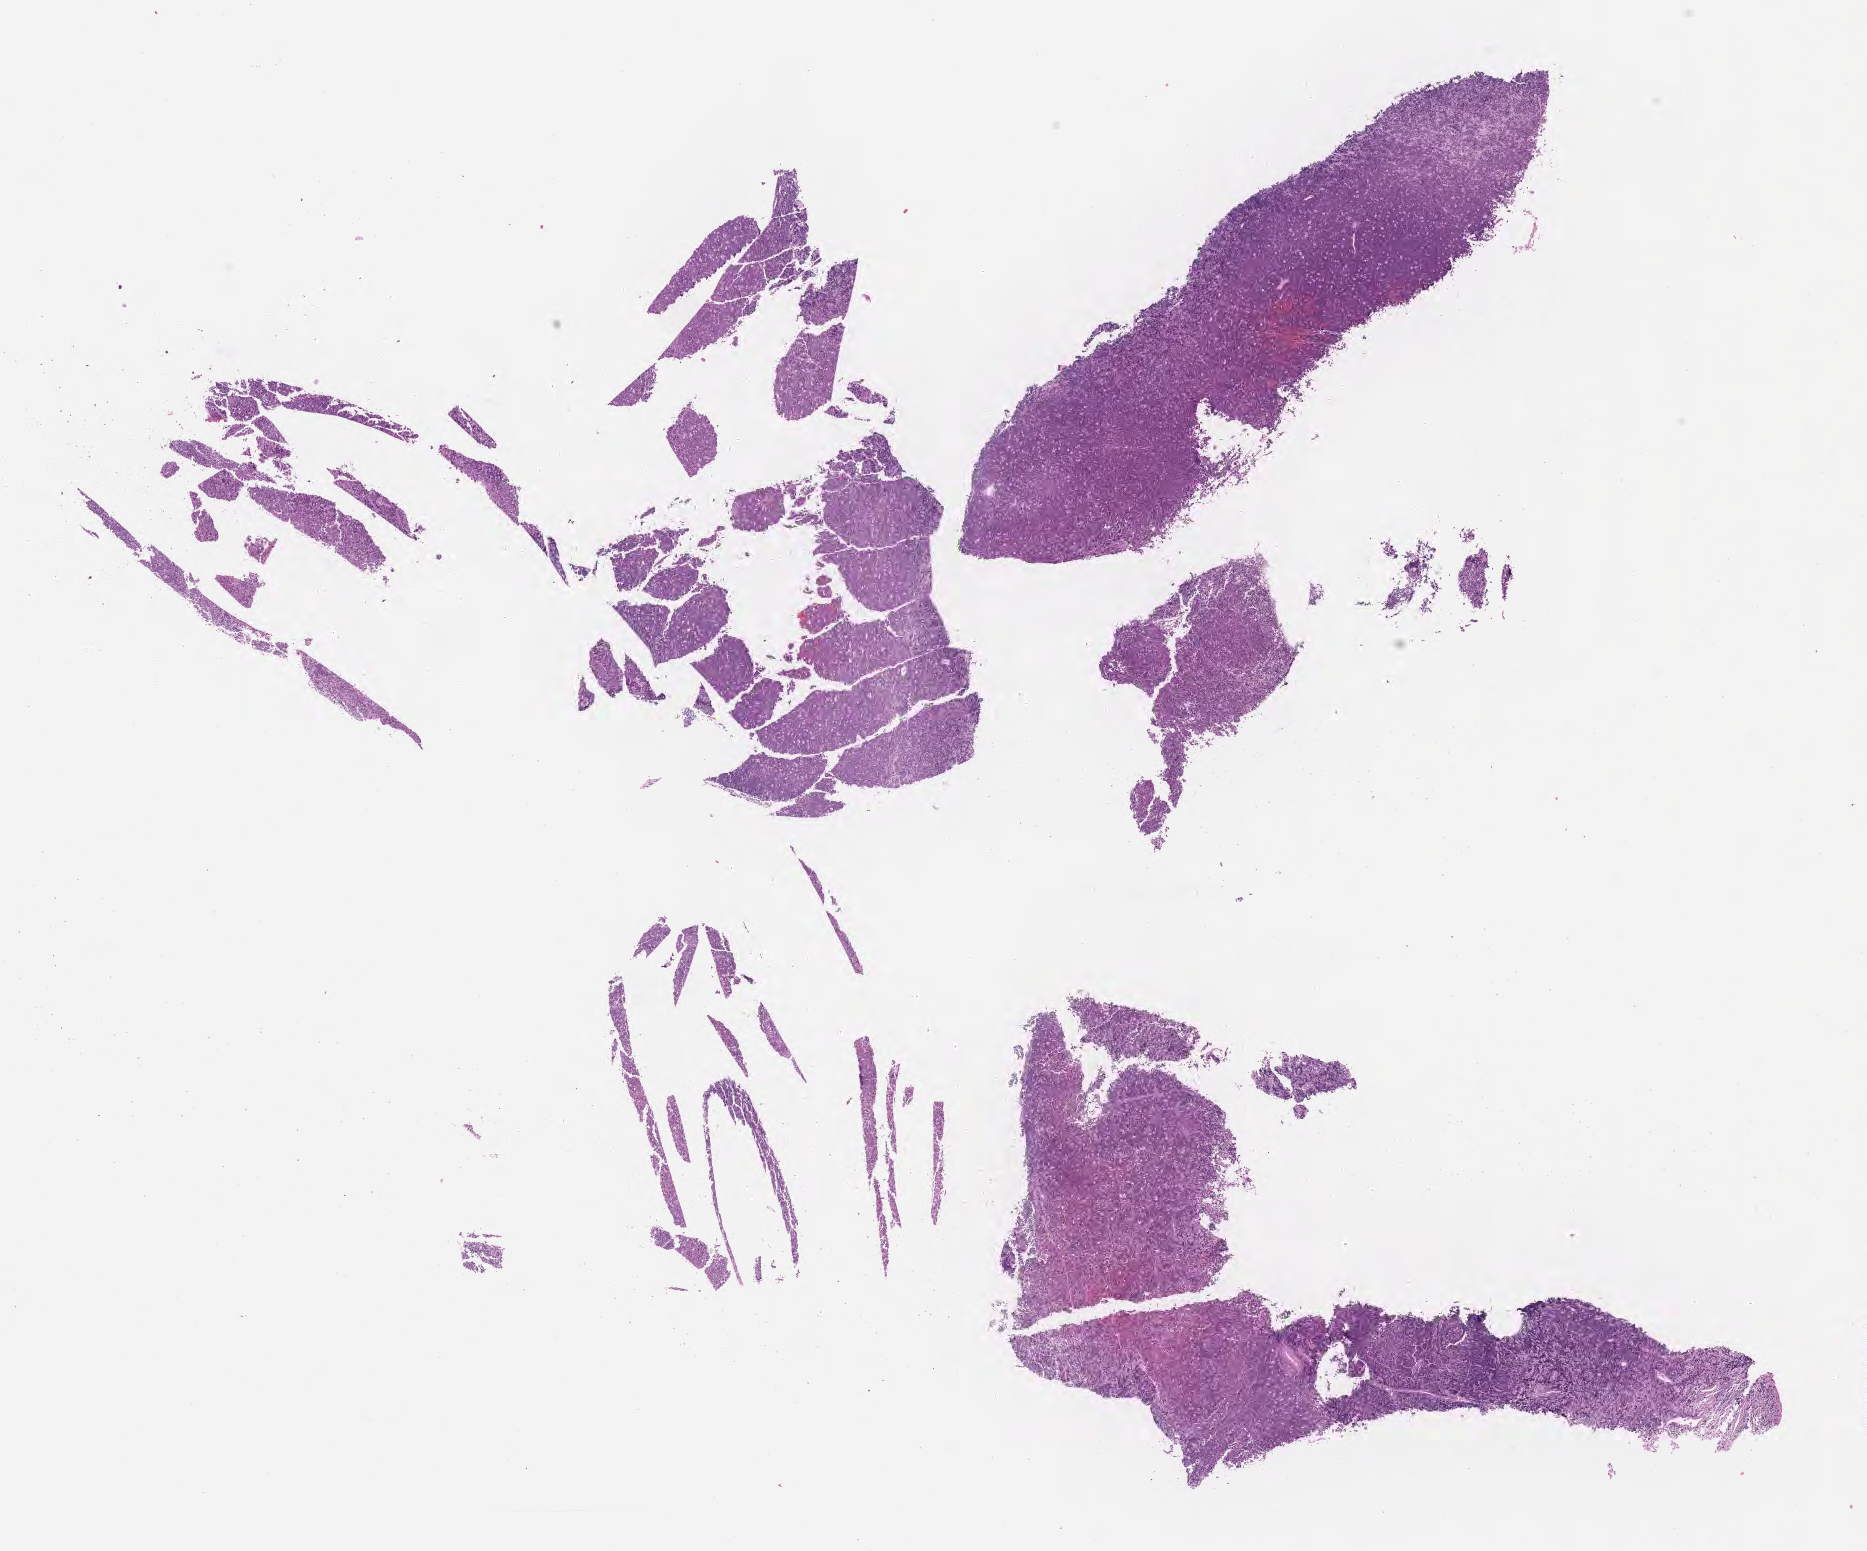
Whole-slide image, haematoxylin and eosin stain — shown as a low-resolution overview of the whole scanned area (about 15.1 x 12.5 mm). FFPE section. Primary tumor. Male patient; age at initial diagnosis 9 years. Composition of this section per pathologist review: tumor cells 90%, tumor nuclei 95%, stromal cells 5%, necrosis 5%, normal cells 0%. Inflammatory infiltration, as recorded: lymphocyte infiltration 30%, monocyte infiltration 30%, neutrophil infiltration 5%.
Ann Arbor stage (patient): Stage IV. Diagnosis: Burkitt lymphoma, NOS.